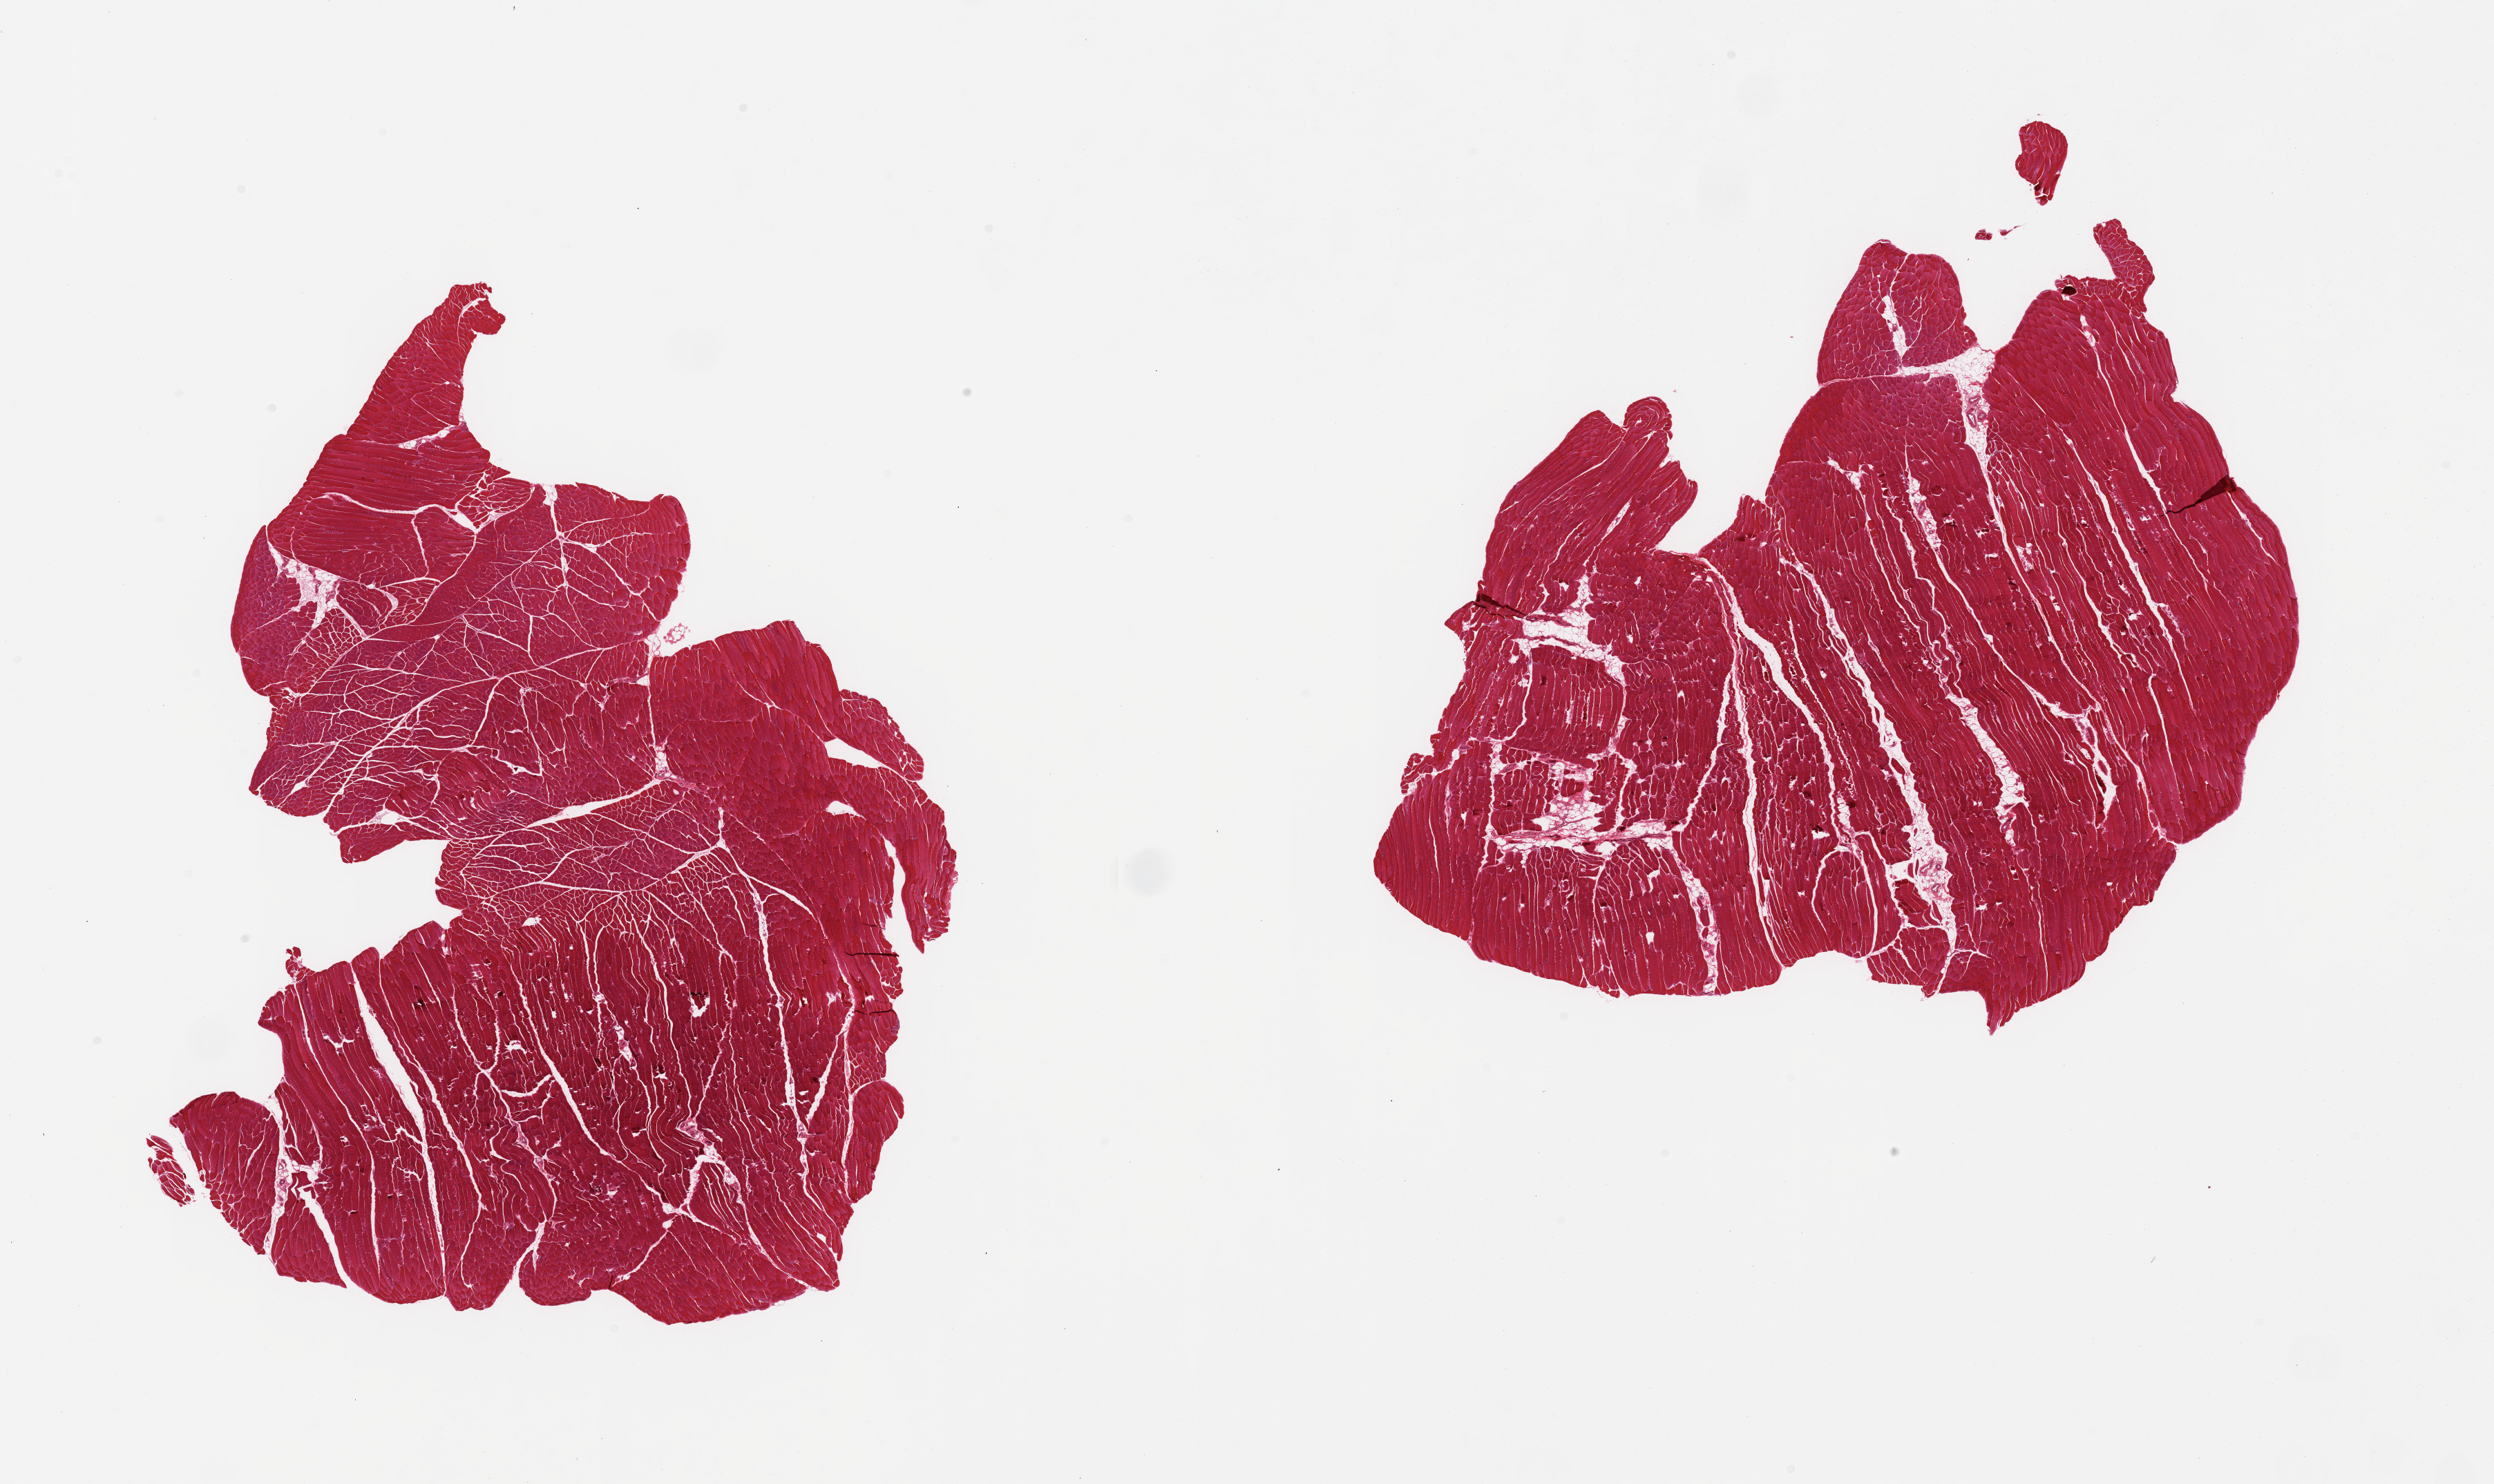
Digitized H&E-stained section — a low-resolution overview of the entire scanned area, about 28.5 x 17.0 mm. PAXgene-fixed, paraffin-embedded tissue. Section of skeletal muscle (target tissue). Tissue donor sample. Female donor.
Review note (as recorded): 2 pieces, 5-10% internal fat.